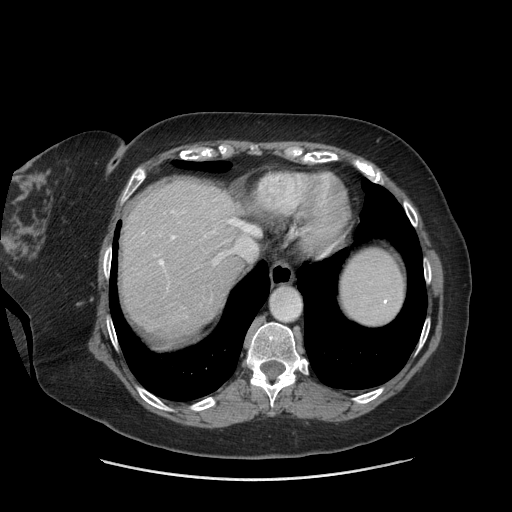
Contrast-enhanced abdominal CT (liver protocol), one axial slice. Position 61 of 69 along the scan axis. Reconstruction kernel STANDARD. 140 kVp. Soft-tissue window (W 400 / L 40 HU). 2.5 mm slice thickness. 512 × 512 image matrix, field of view 420 × 420 mm. From the clinical record (not read from this slice): diagnosis: hepatocellular carcinoma (patient treated with transarterial chemoembolisation; whether this scan precedes or follows treatment is not stated here); TNM stage (as recorded): Stage-IIIB; Child-Pugh class: A; tumour differentiation: moderately differentiated; tumour nodularity: multinodular.
Outlined on this slice (semi-automatic segmentation, software-assisted and operator-edited):
- abdominal aorta: bounding box [x1, y1, x2, y2] px = [271, 288, 300, 320]
- liver parenchyma outside the tumour (the mass and vessels are separate outlines, so this box may not span the whole liver): [120, 180, 244, 336]
- mass: [147, 306, 188, 342]
- liver vessels: [143, 211, 242, 266]